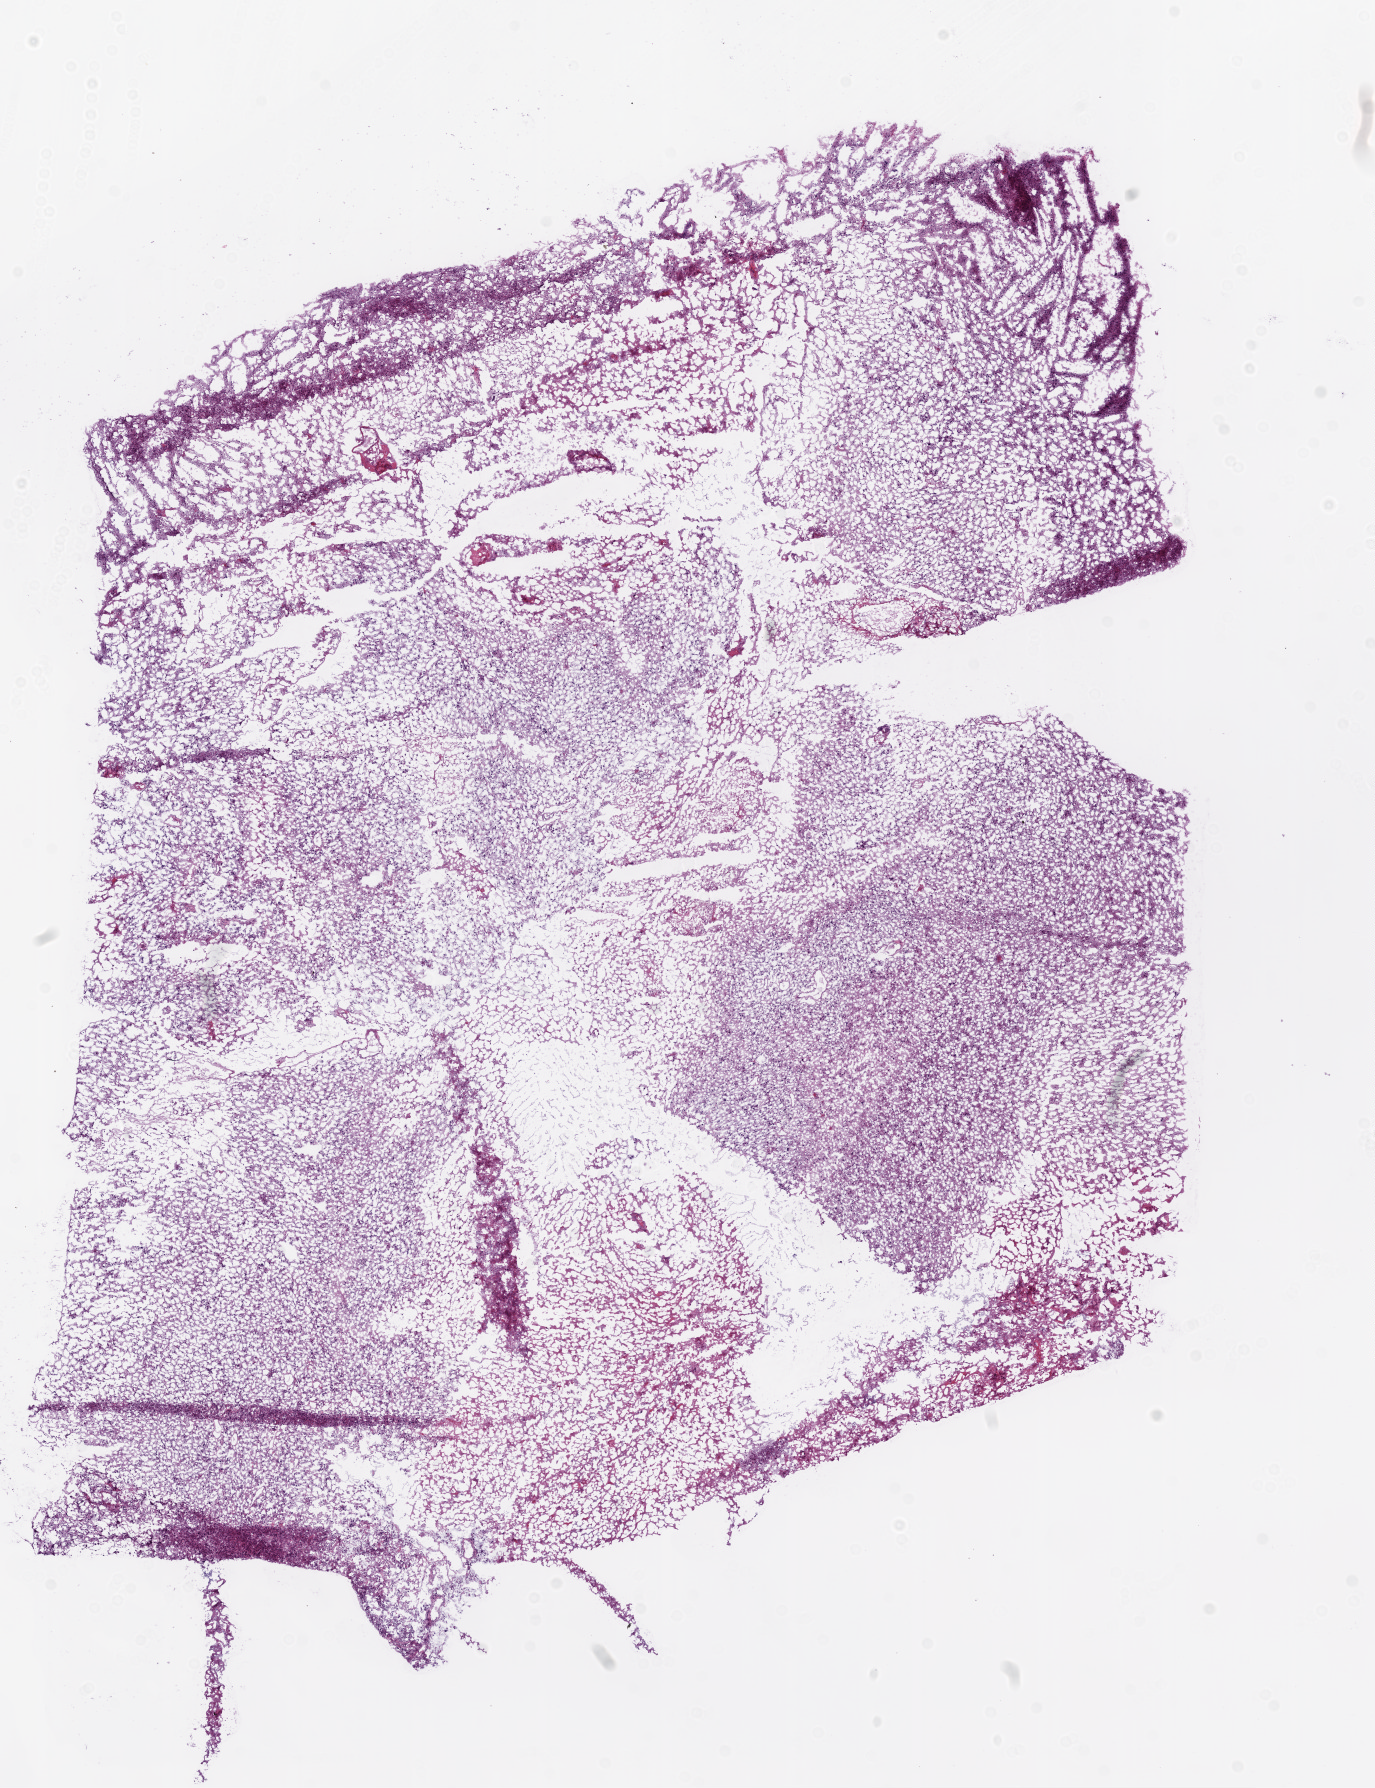
Whole-slide histology image, H&E-stained, whole scanned area (about 11.0 x 14.3 mm, acquisition: 20x scan) shown as a low-resolution overview. Frozen section from the bottom of the tissue portion. Primary tumour sample from the brain. Female patient; age at initial diagnosis 76 years.
Histologic diagnosis: Glioblastoma.